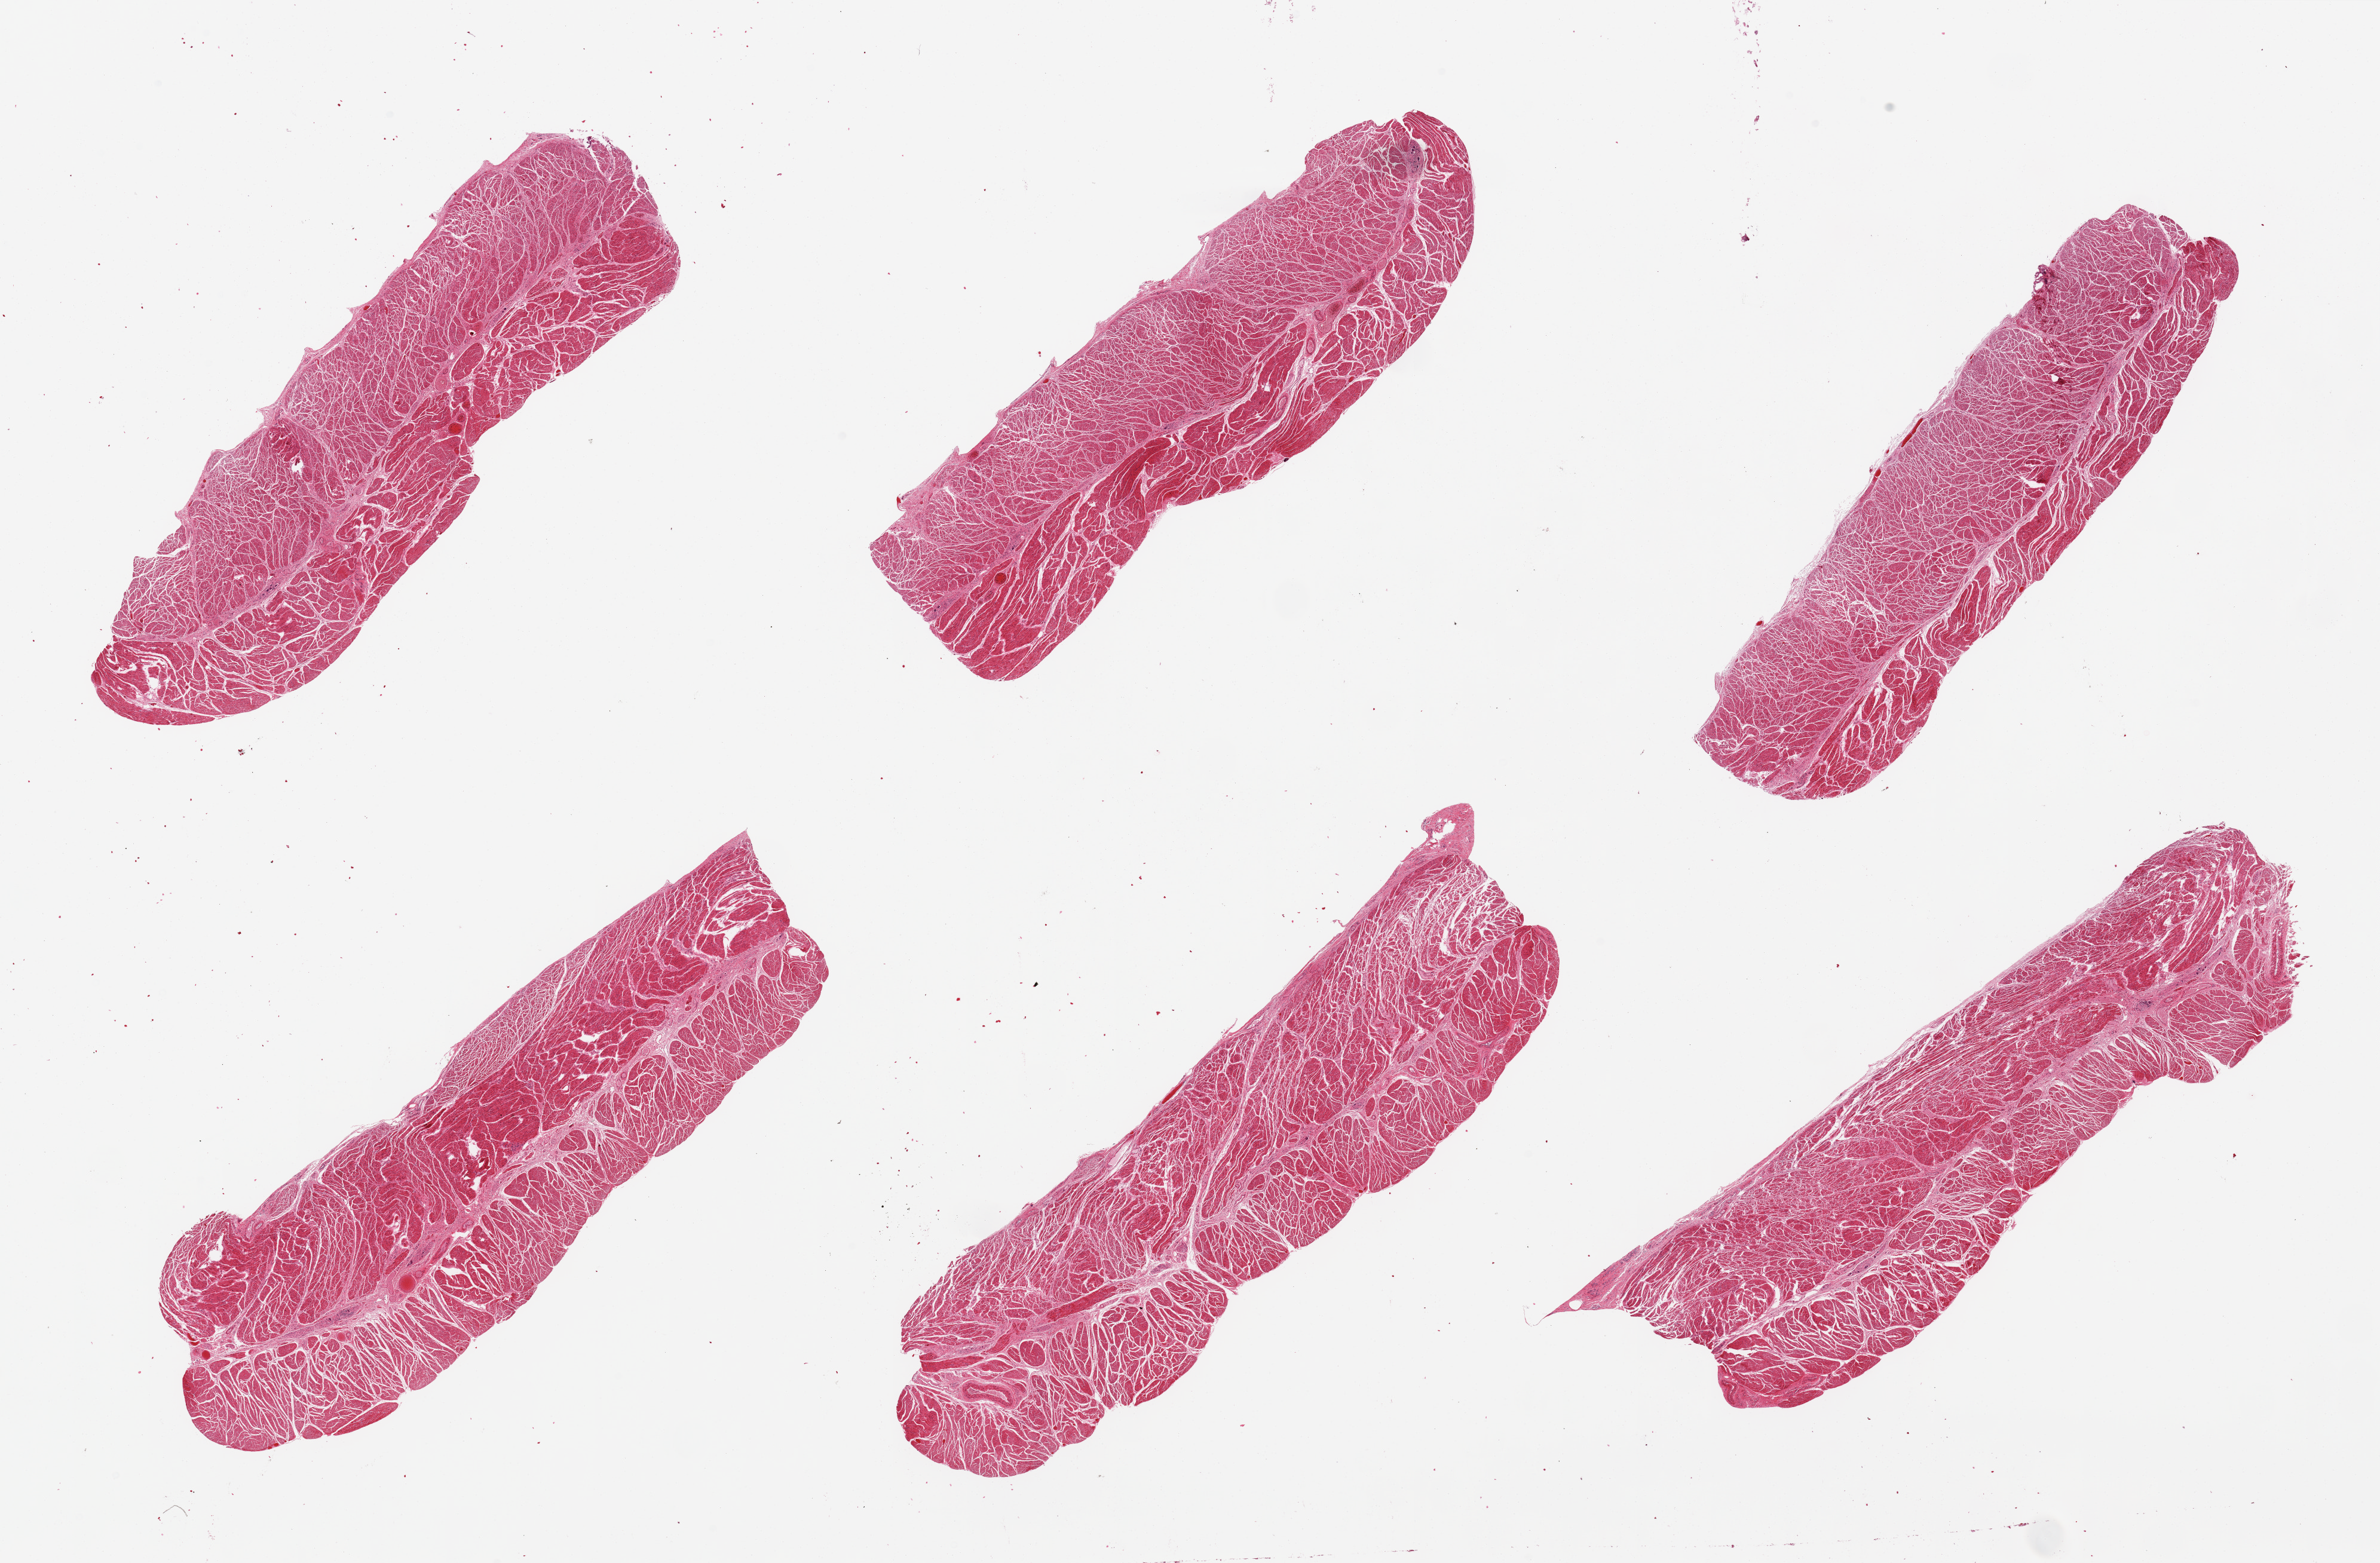
Whole-slide image, haematoxylin and eosin stain, brightfield, a low-resolution overview of the entire scanned area, about 31.5 x 20.7 mm (acquisition: 20x scan), PAXgene-fixed paraffin-embedded (PFPE) section, section of gastroesophageal junction (target tissue), donor tissue sample. Male donor.
• reviewer comment on this tissue sample: 6 pieces; well dissected muscularis